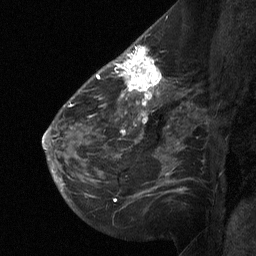
Breast MRI (dynamic contrast-enhanced), one sagittal slice; position 39 of 64 along the scan axis; dynamic contrast-enhanced study with each time point stored as its own series, time point 2 of 3 at this slice position (early post-contrast, ordered by acquisition time); 1.5 T; TE 4.8 ms, TR 27 ms; 256 × 256 image matrix, field of view 200 × 200 mm. Female patient, age 51 years. From the clinical record (not read from this slice): setting: breast cancer imaged before/during neoadjuvant chemotherapy; receptor status: HR-positive, HER2-negative.
Outlined on this slice (semi-automatically segmented with operator editing):
- analysis volume of interest (the breast-tissue region the enhancement analysis was run in; not a lesion): bounding box [x1, y1, x2, y2] px = [112, 46, 169, 106]
- tumour enhancement mask (voxels above the 90 % enhancement threshold inside the analysis volume of interest): [118, 46, 162, 106]